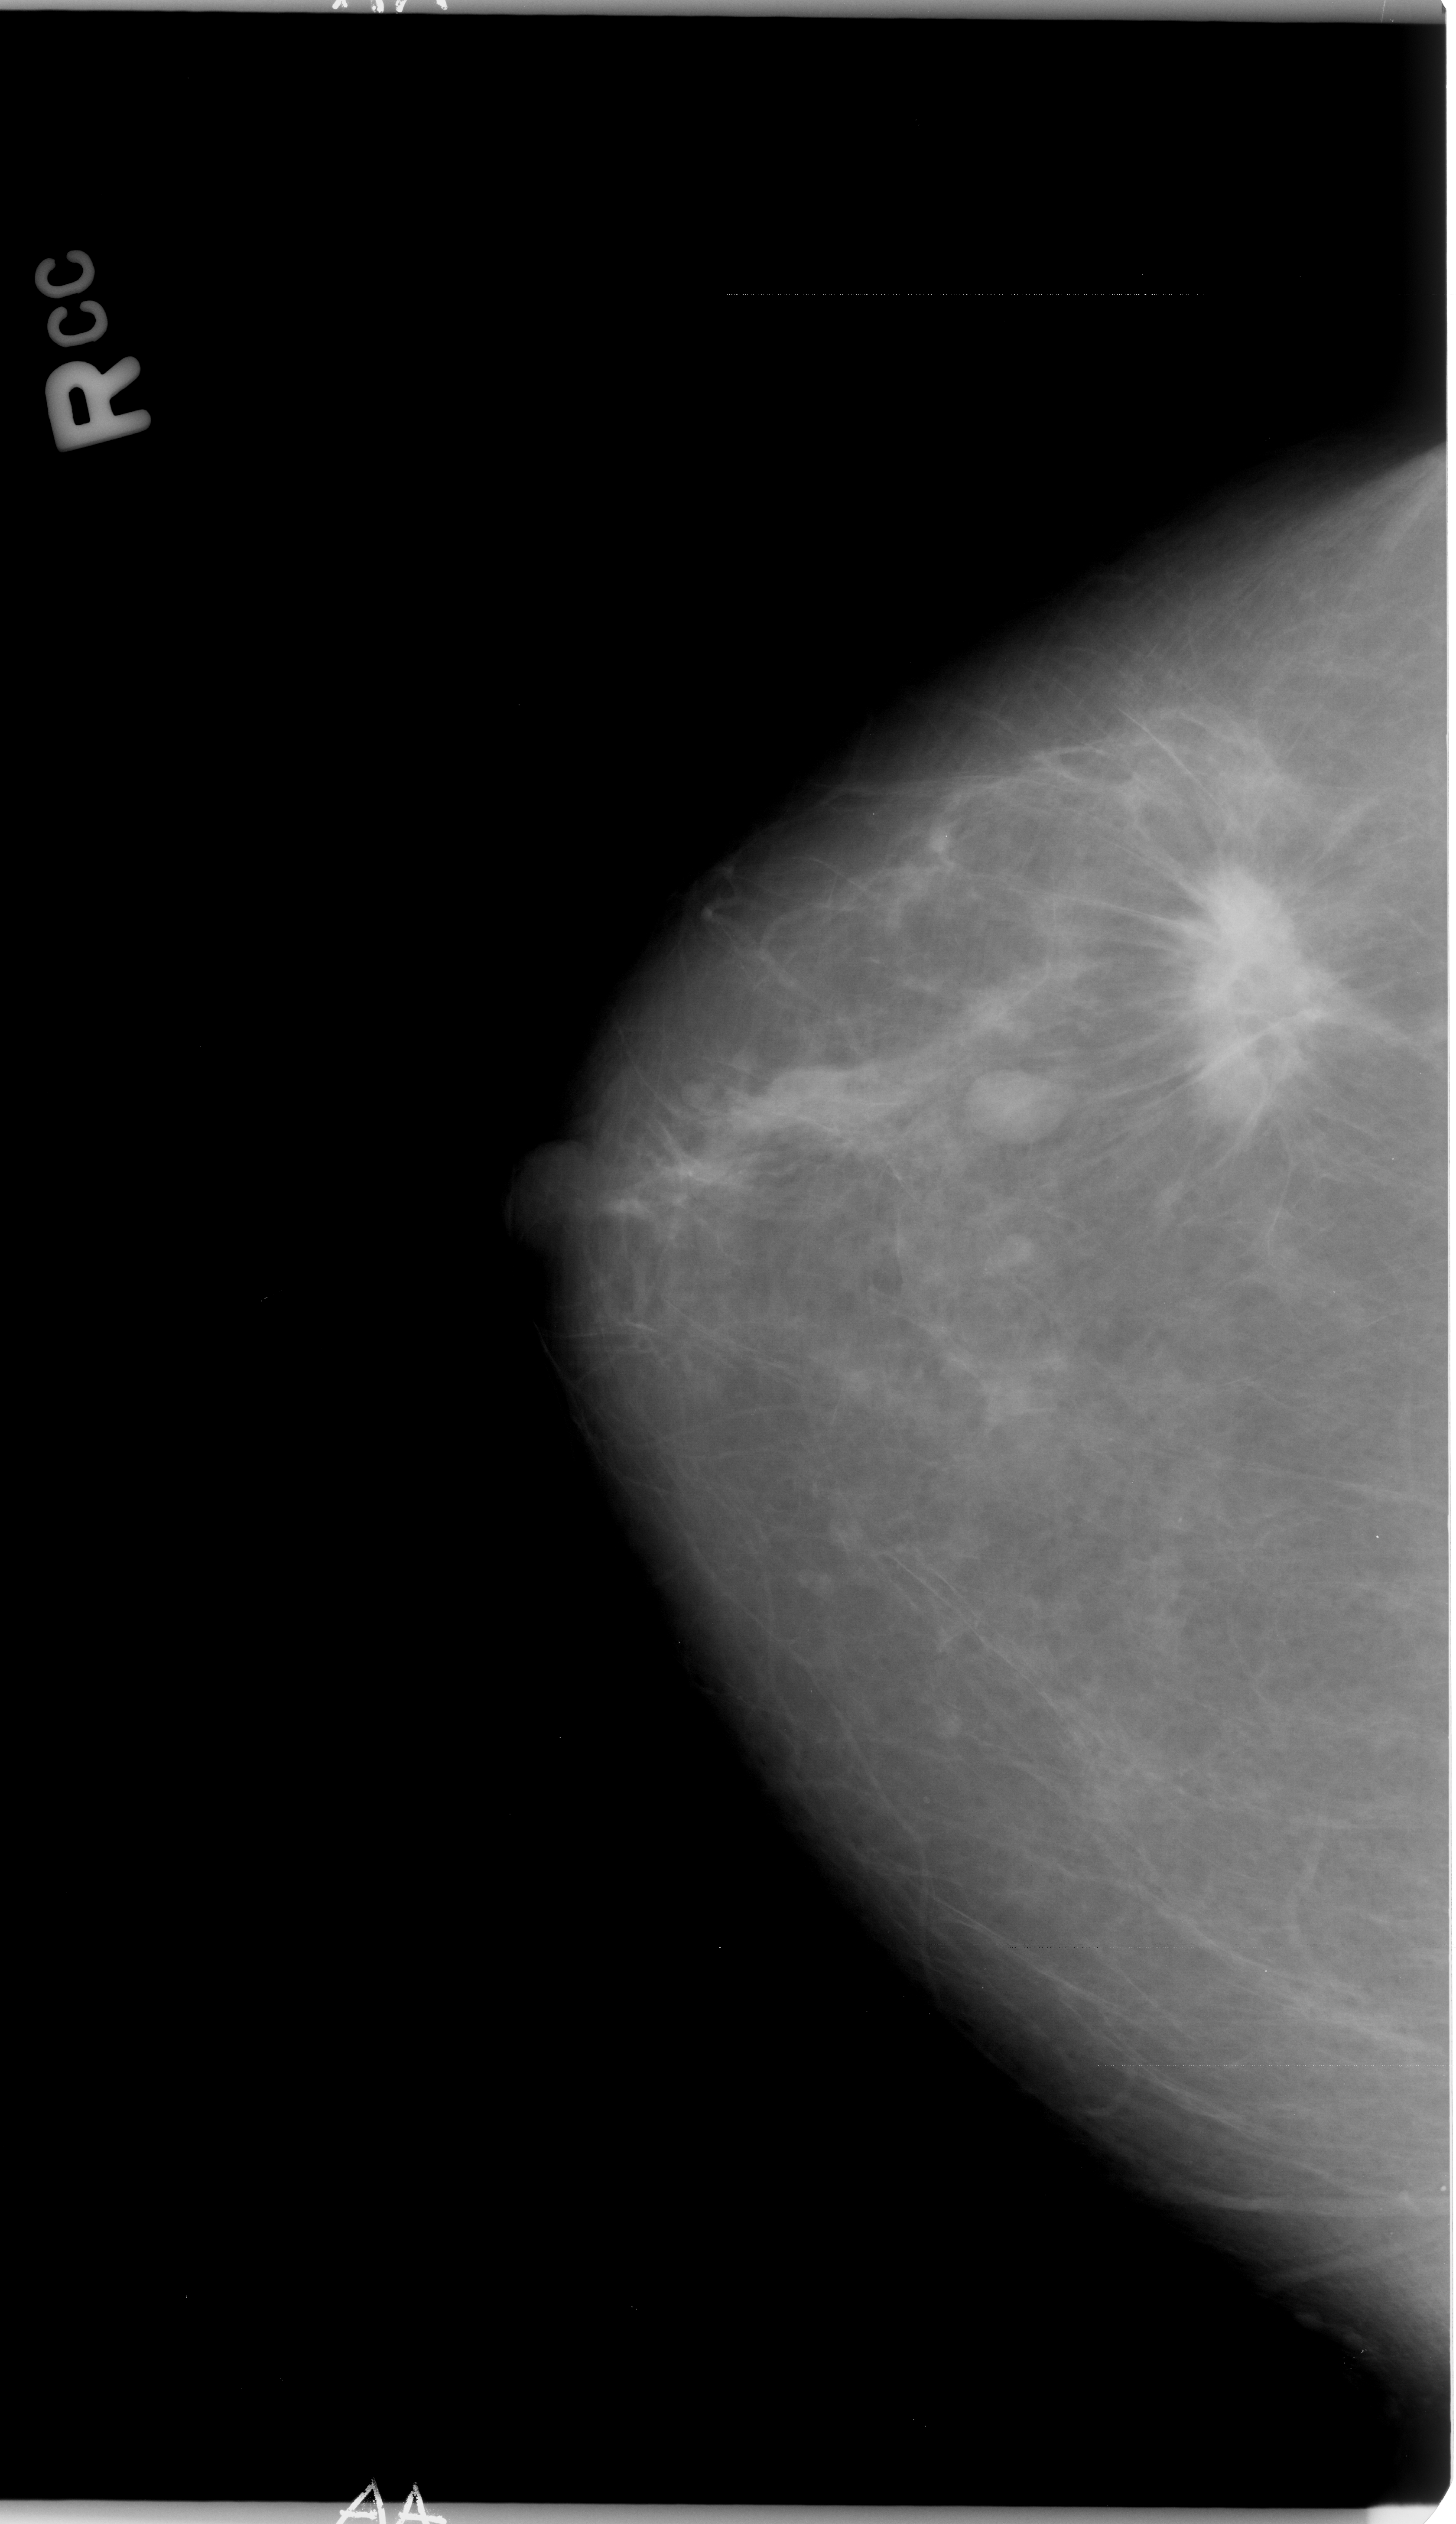
Digitized screen-film mammogram. Right breast. Craniocaudal (CC) view. 1456 × 2524 image matrix.
Marked abnormalities (boxes around the expert regions of interest):
- mass, shape irregular / architectural distortion, margins spiculated; BI-RADS assessment category 5; pathology (as recorded): malignant: bounding box <1168,871,1377,1085> (left, top, right, bottom; pixels)